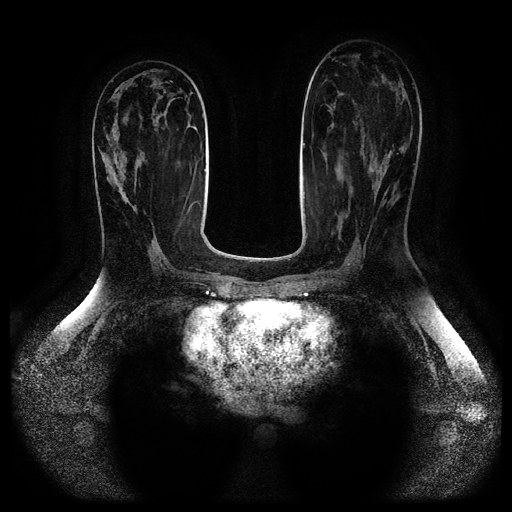
Breast MRI (dynamic contrast-enhanced, multi-phase), one axial slice; position 44 of 116 along the scan axis; dynamic contrast-enhanced series, time point 2 of 5 at this slice position (early post-contrast); 1.5 T; TE 2.6 ms, TR 5.2 ms; 2 mm slice thickness; 512 × 512 image matrix, field of view 380 × 380 mm. Patient: female, 44 years.
Structures marked on this image (semi-automatically segmented with operator editing):
- breast lesion (labelled benign in the annotation): box from (x=99, y=113) to (x=140, y=208) px